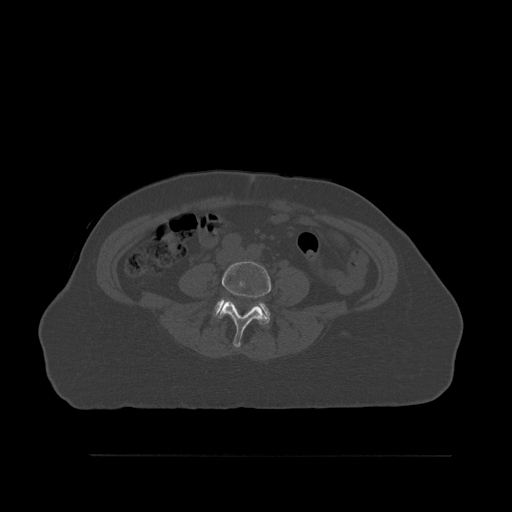
CT including the spine, one axial slice; position 203 of 527 along the scan axis; bone window (W 1800 / L 400 HU); 1.5 mm slice thickness; 512 × 512 image matrix, field of view 470 × 470 mm. Patient: female, 73 years. From the clinical record (not read from this slice): primary cancer: breast; vertebrae with lytic lesions (as recorded): L2.
Structures marked on this image (semi-automatically segmented with operator editing):
- L4 vertebra: box from (x=218, y=261) to (x=271, y=347) px
- L5 vertebra: (x=213, y=298)–(x=270, y=325)